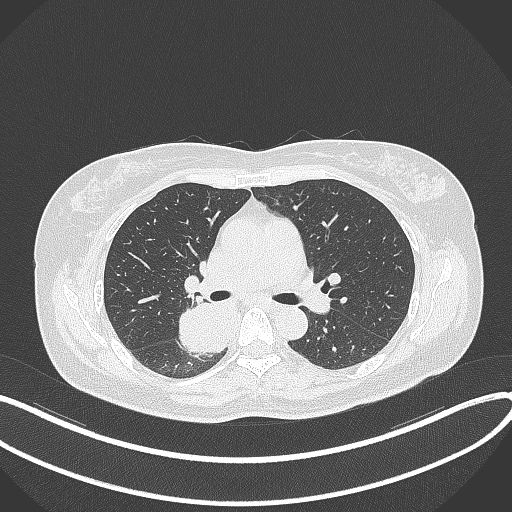
Chest CT, one axial slice; position 219 of 331 along the scan axis; lung window (W 1500 / L -600 HU); 1 mm slice thickness; 512 × 512 image matrix, field of view 400 × 400 mm. Patient: female, 54 years. From the clinical record (not read from this slice): clinical TNM (as recorded): T4 N0 M0.
Annotated regions visible in this slice (rectangle marked by the reading radiologist):
- lung tumour (recorded histology: adenocarcinoma): box from (x=176, y=298) to (x=234, y=357) px